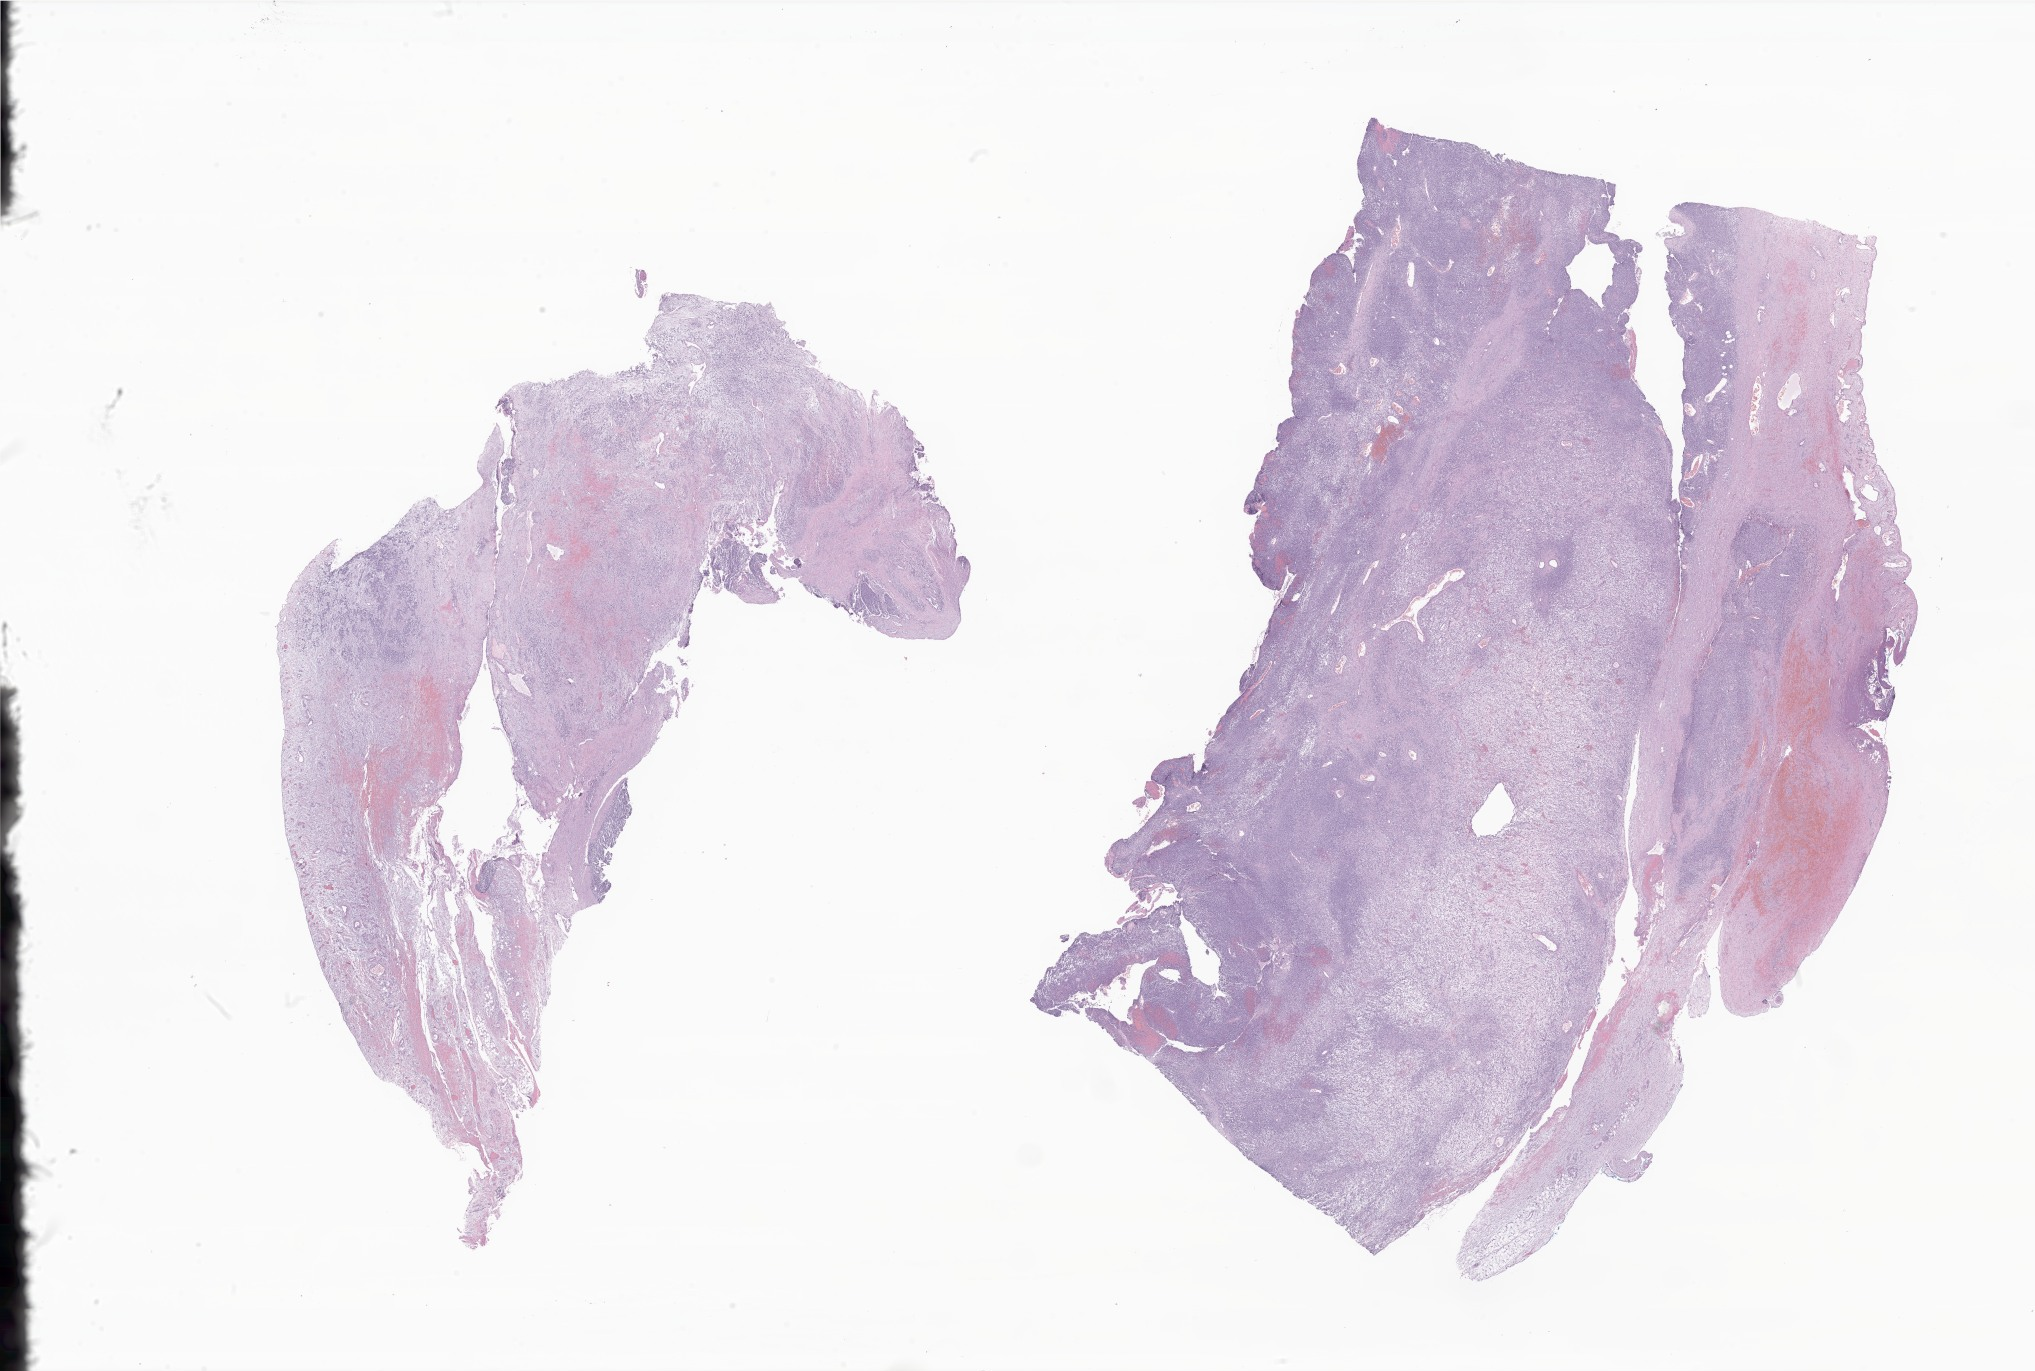
Whole-slide image, H&E stain of tumor tissue from the abdomen, shown as a low-resolution overview of the whole scanned area (about 34.3 x 23.1 mm). Formalin-fixed paraffin-embedded section. Patient female; age 637 days (about 1.7 years).
Diagnosis (ICD-O-3 morphology term): Embryonal rhabdomyosarcoma, NOS.